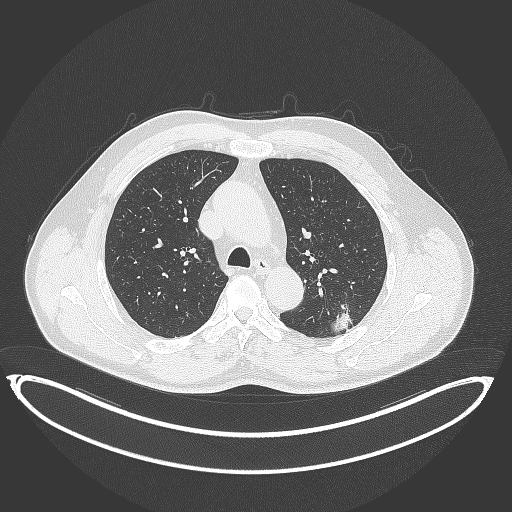
Chest CT, one axial slice; position 251 of 399 along the scan axis; lung window (W 1500 / L -600 HU); 1 mm slice thickness; 512 × 512 image matrix. Patient: male, 58 years. From the clinical record (not read from this slice): clinical TNM (as recorded): T1c N0 M0; histopathological grade: G1-2.
Structures marked on this image (rectangle marked by the reading radiologist):
- lung tumour (recorded histology: adenocarcinoma): bounding box [x1, y1, x2, y2] px = [325, 300, 360, 334]